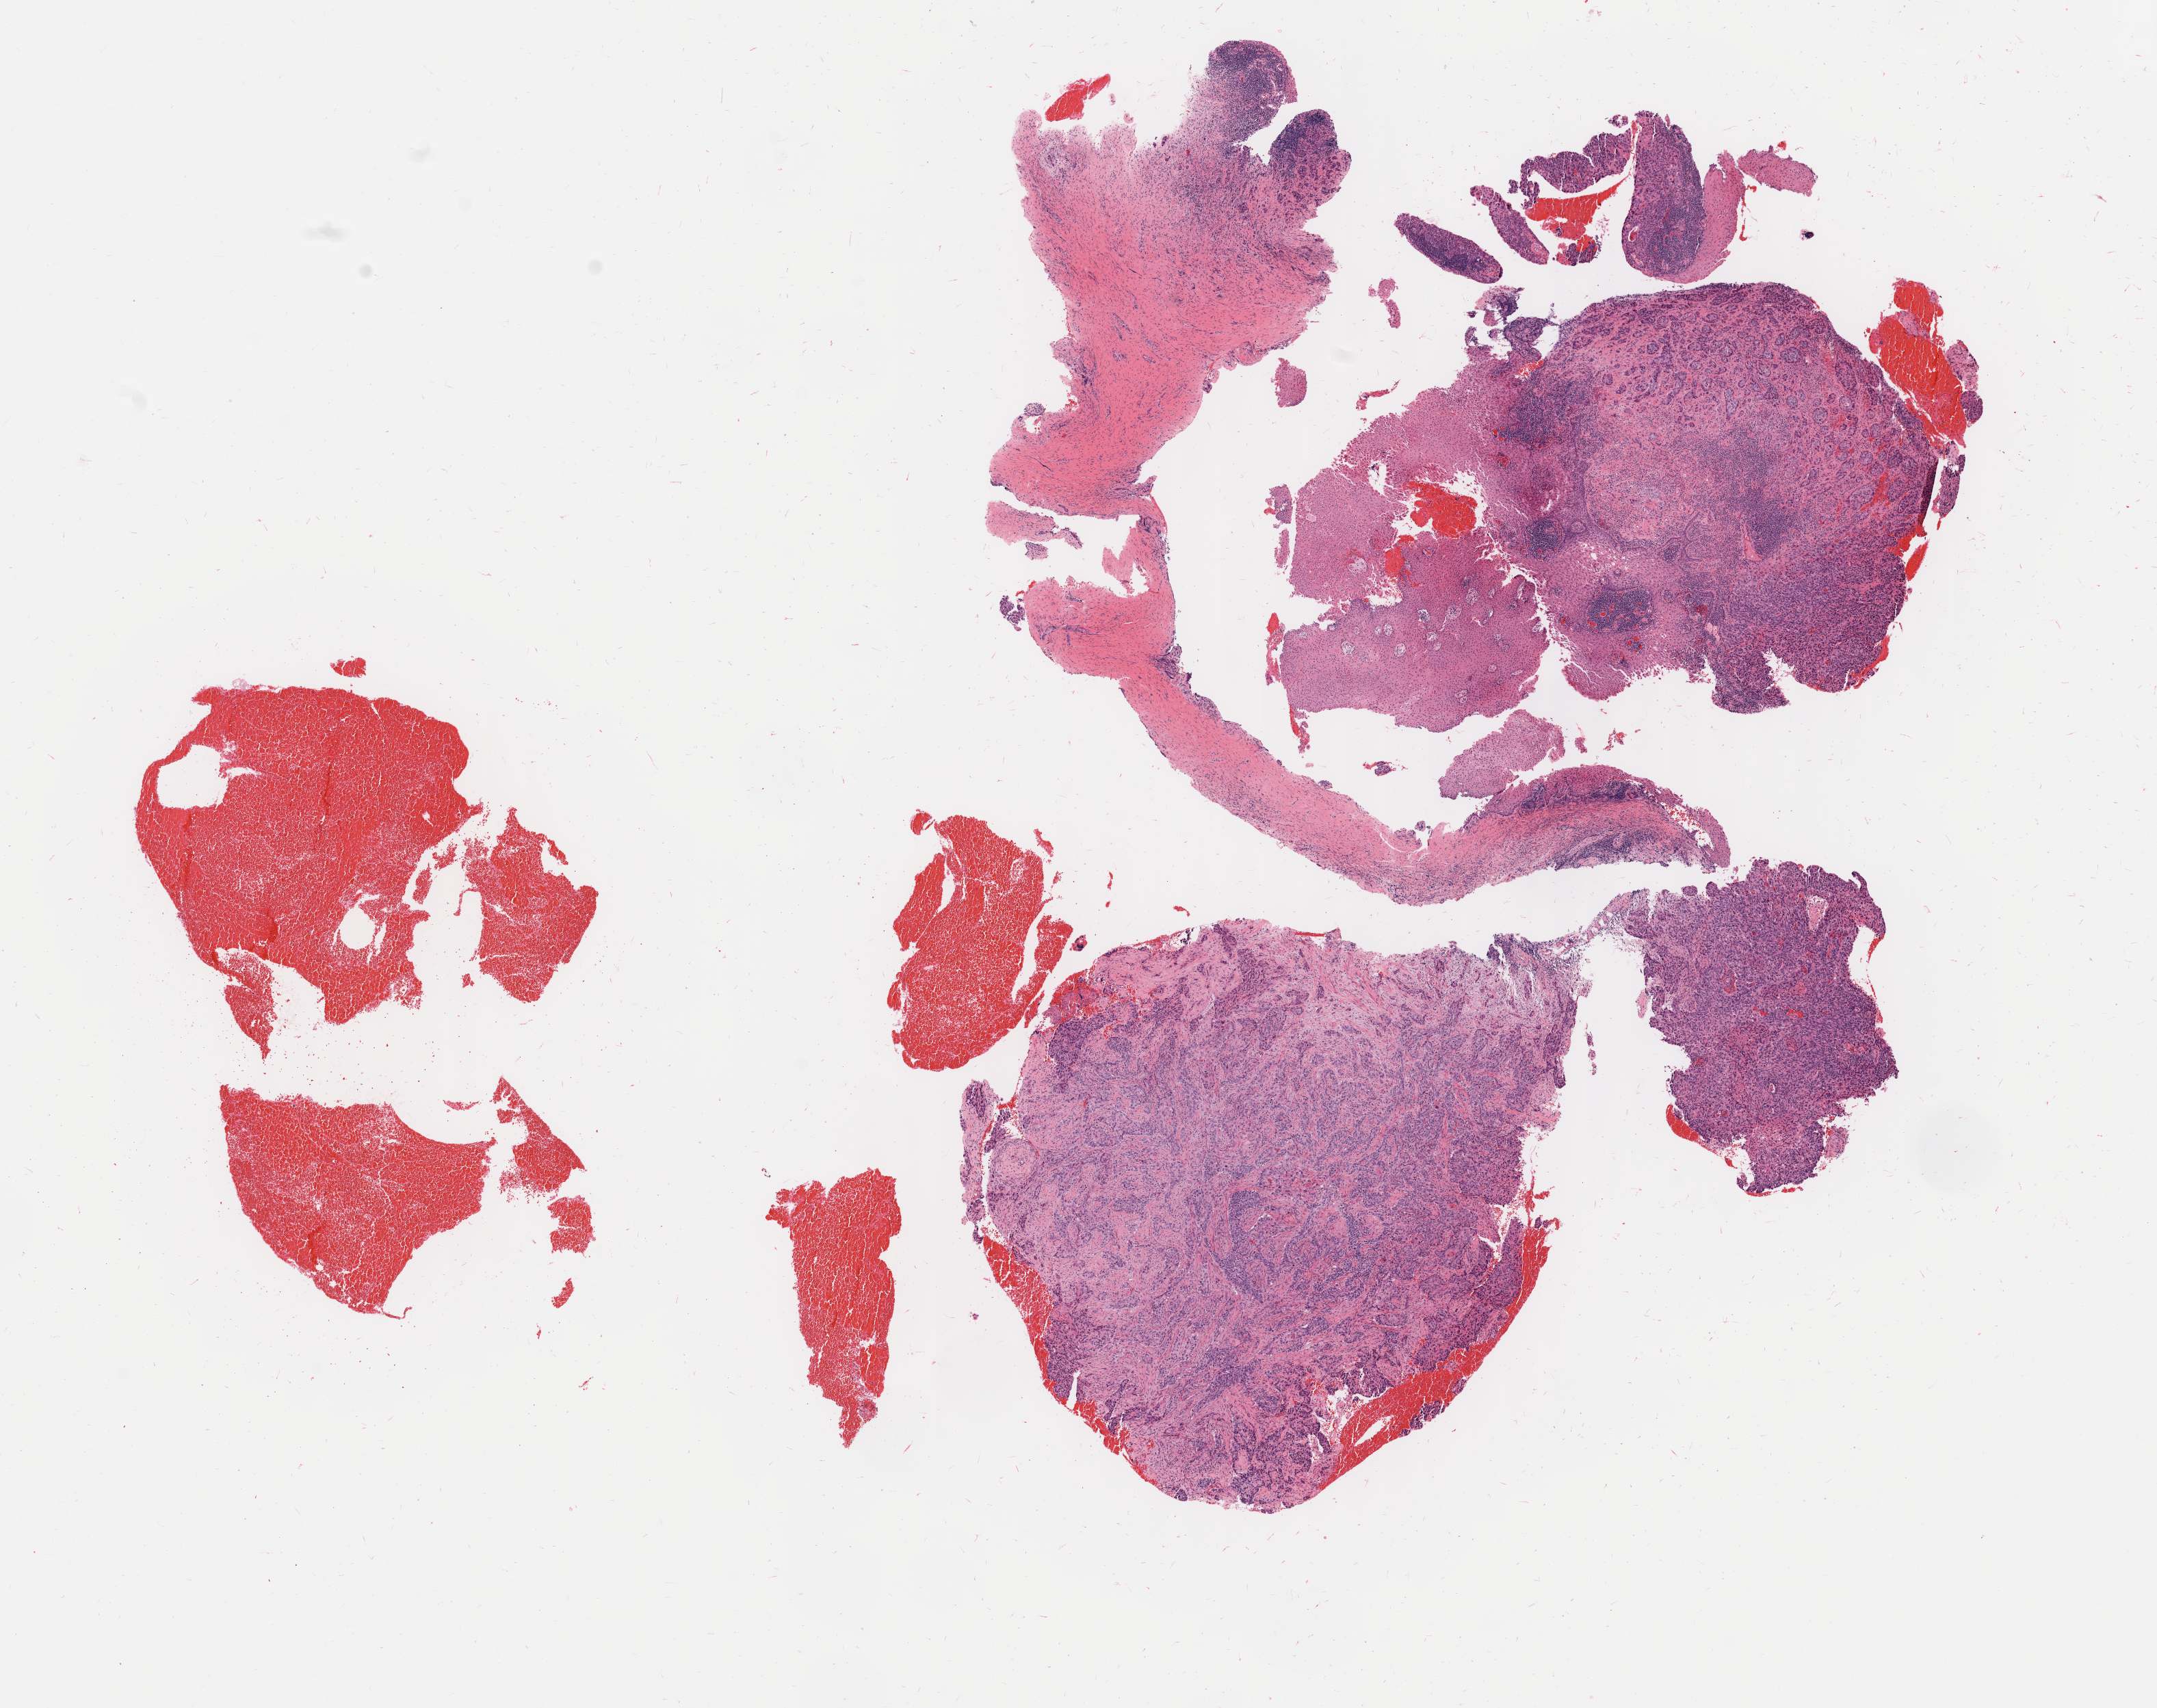
H&E whole-slide image, a low-resolution overview of the entire scanned area, about 12.5 x 9.9 mm. Specimen: tumor tissue. Site: cervix. Female patient, aged 47.
• histologic diagnosis: Squamous cell carcinoma, large cell, nonkeratinizing, NOS